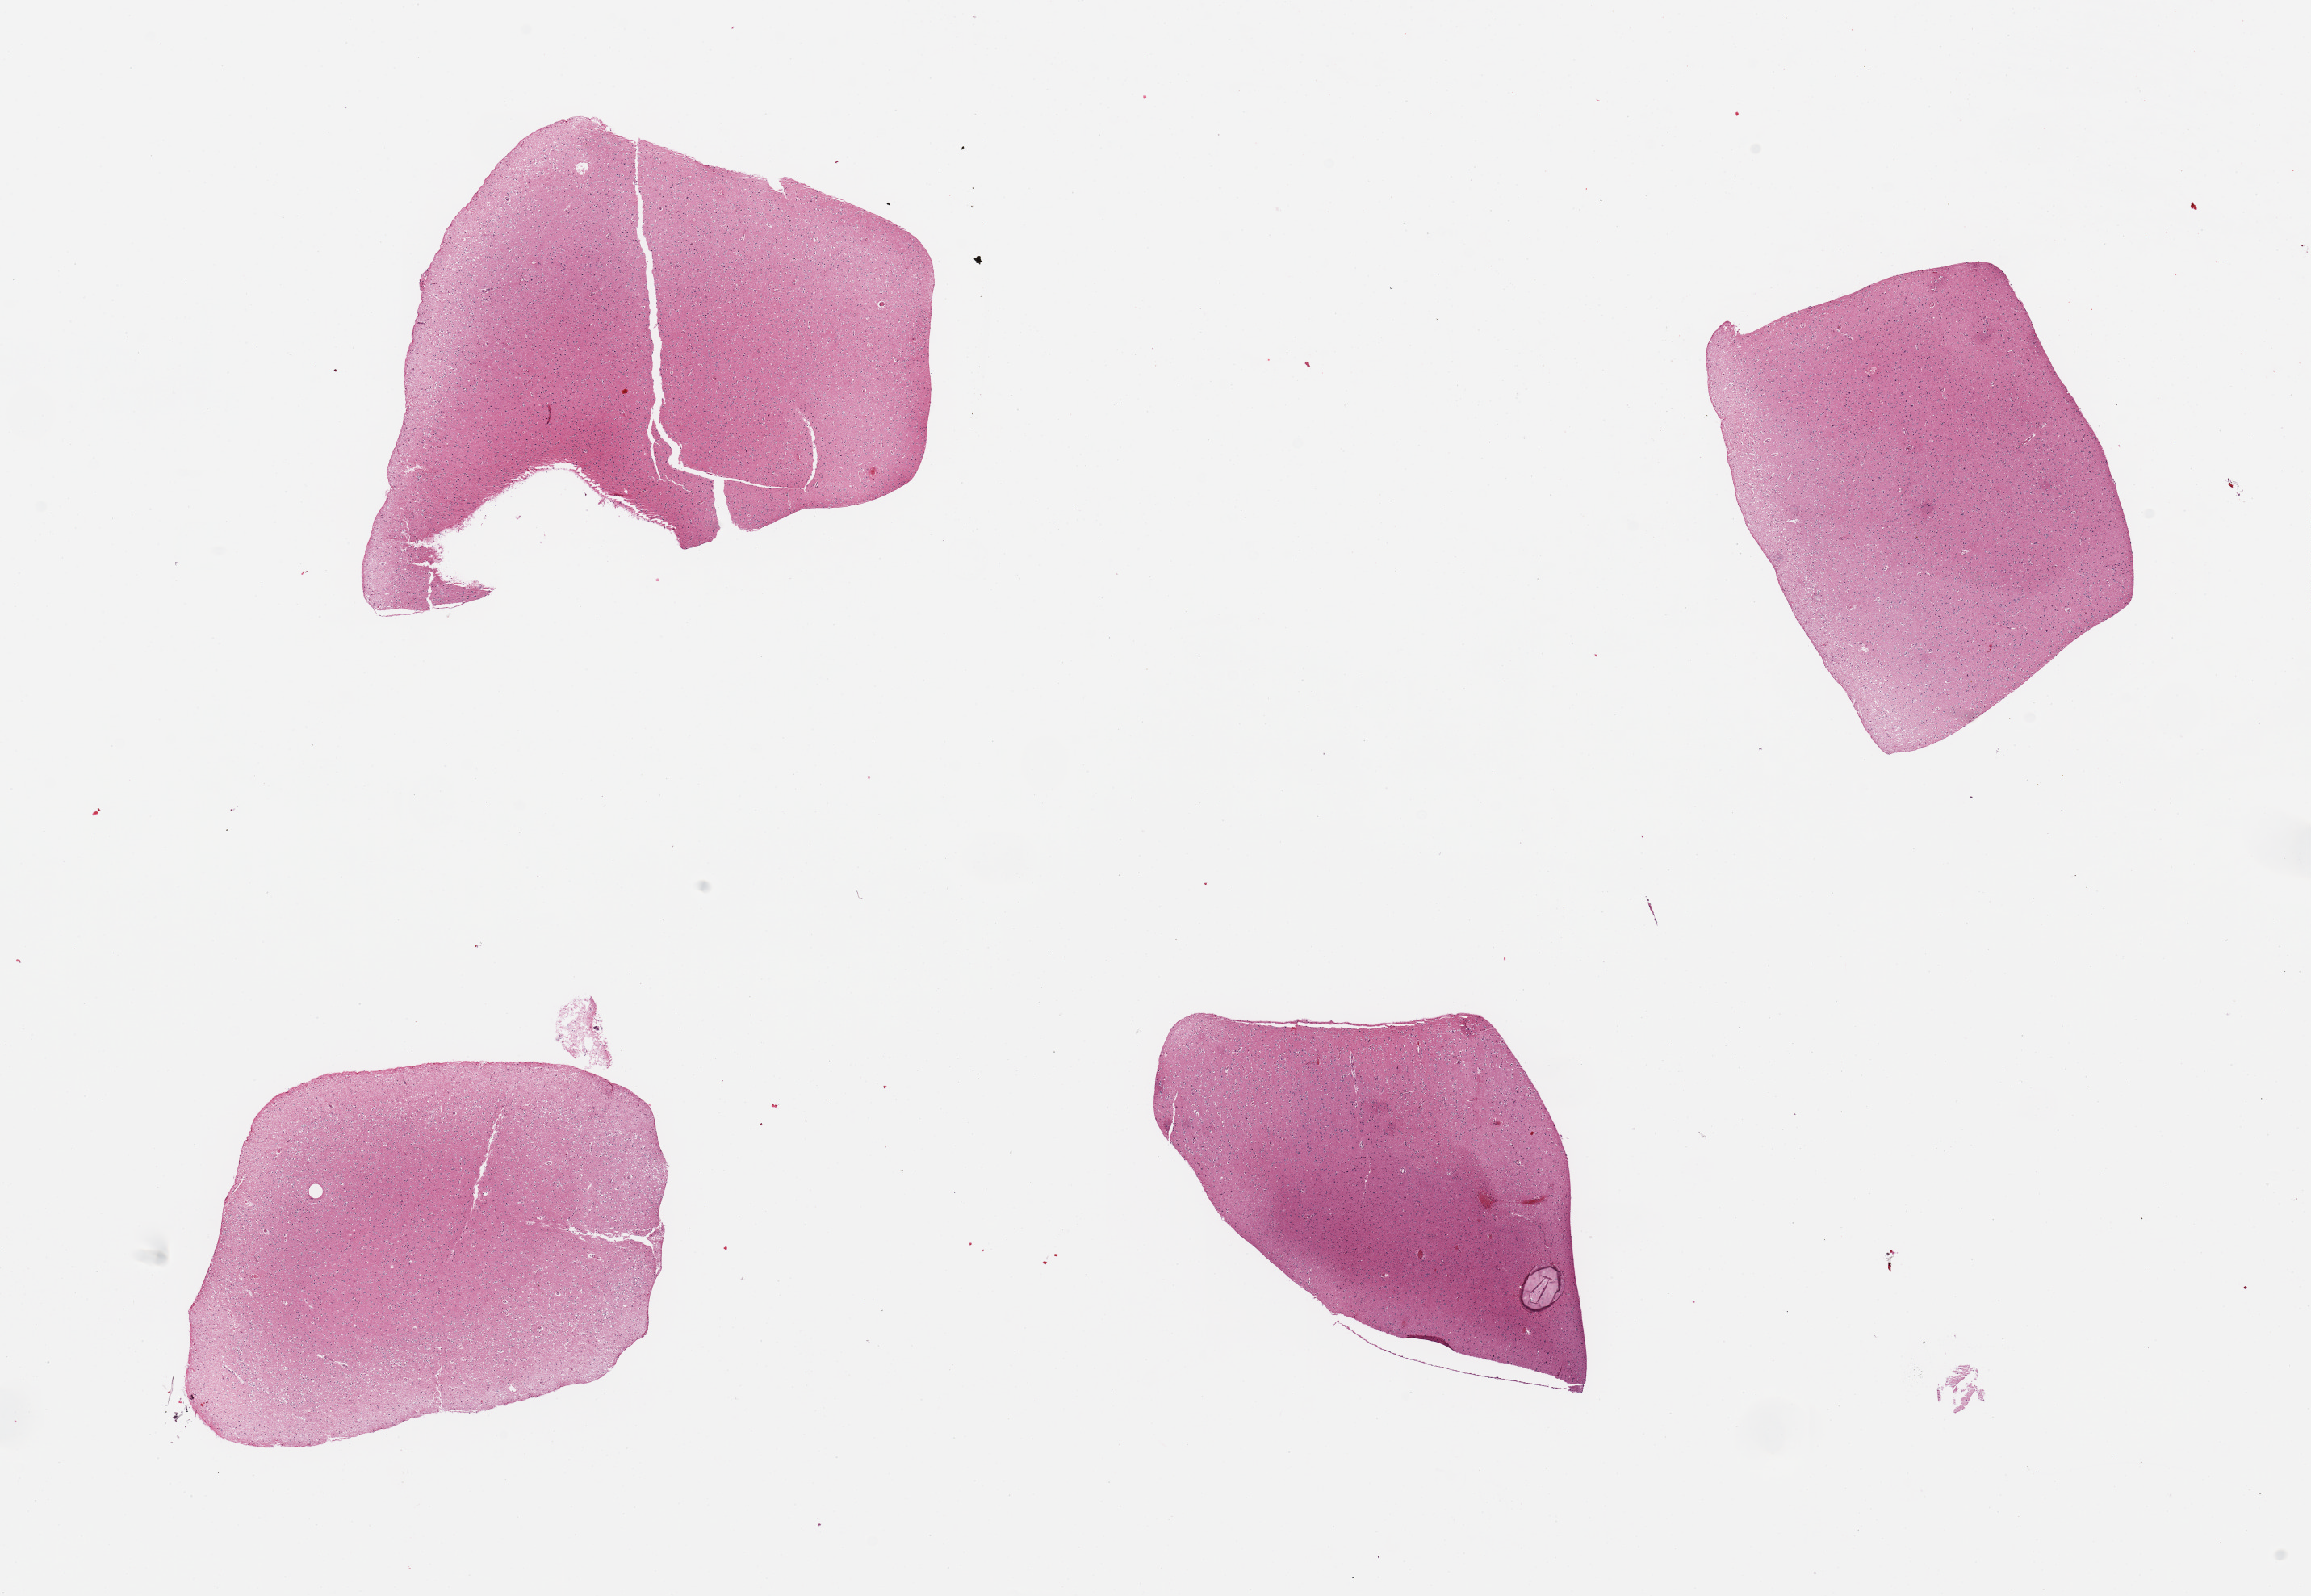
H&E whole-slide image, shown as a low-resolution overview of the whole scanned area (about 22.6 x 15.6 mm, slide scanned at 20x); PAXgene-fixed, paraffin-embedded tissue; target tissue: cerebral cortex; tissue donor sample. Donor: male.
- pathologist's review note for this sample: 4 pieces, no abnormalities